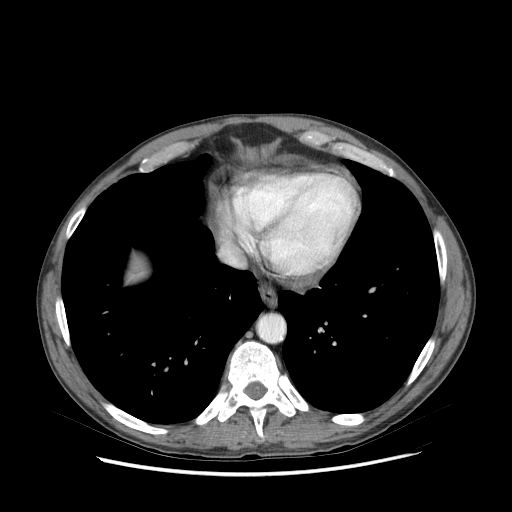
Contrast-enhanced abdominal CT (liver protocol), one axial slice; slice 77 of 89 in the series (ordered by position); reconstruction kernel STANDARD; 140 kVp; soft-tissue window (W 400 / L 40 HU); 2.5 mm slice thickness; 512 × 512 image matrix. From the clinical record (not read from this slice): diagnosis: hepatocellular carcinoma (patient treated with transarterial chemoembolisation; whether this scan precedes or follows treatment is not stated here); TNM stage (as recorded): Stage-IIIB; Child-Pugh class: A; tumour nodularity: multinodular.
Annotated regions visible in this slice (semi-automatic segmentation, software-assisted and operator-edited):
- liver parenchyma outside the tumour (the mass and vessels are separate outlines, so this box may not span the whole liver): bounding box [x1, y1, x2, y2] px = [128, 260, 146, 280]